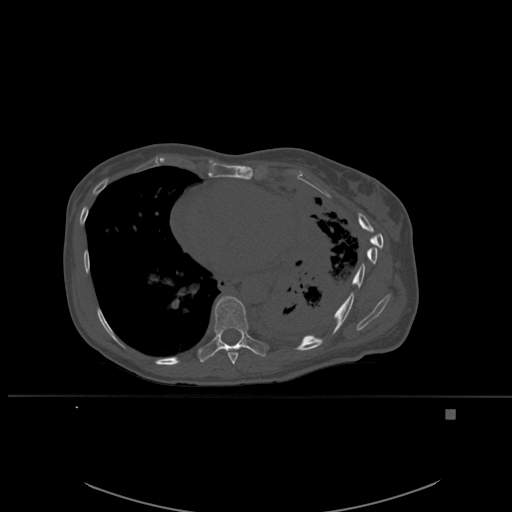
CT including the spine, one axial slice; slice 338 of 537 in the series (ordered by position); bone window (W 1800 / L 400 HU); 1.5 mm slice thickness; 512 × 512 image matrix. Patient: female, 45 years. Case-level facts recorded for this patient, not image findings: primary cancer: lung.
Annotated regions visible in this slice (semi-automatically segmented with operator editing):
- T8 vertebra: bounding box <227,349,238,365> (left, top, right, bottom; pixels)
- T9 vertebra: <198,296,268,362>